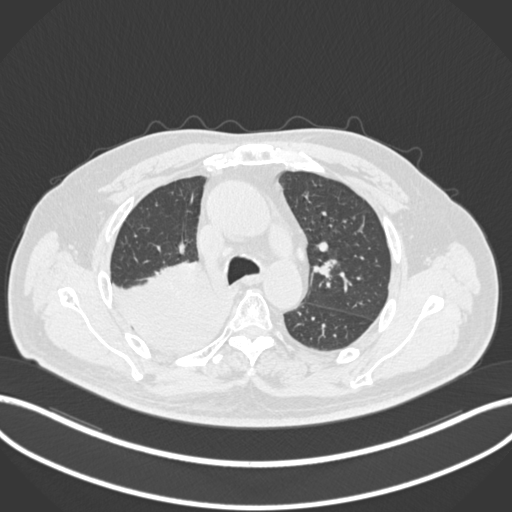
Chest CT, one axial slice. Slice 139 of 218 in the series (ordered by position). Reconstruction kernel B30f. 120 kVp. Lung window (W 1500 / L -600 HU). 1 mm slice thickness. 512 × 512 image matrix, field of view 400 × 400 mm. Male patient, age 68 years. Case-level facts recorded for this patient, not image findings: clinical TNM (as recorded): T2a N0 M0.
Annotated regions visible in this slice (bounding box drawn by a radiologist):
- lung tumour (recorded histology: adenocarcinoma): bounding box [x1, y1, x2, y2] px = [110, 257, 229, 355]